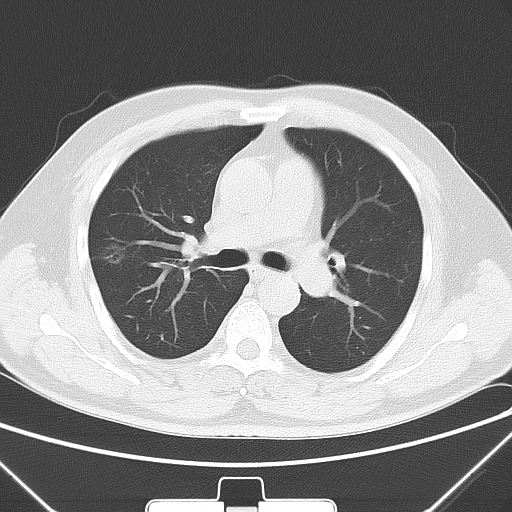
Chest CT, one axial slice; position 39 of 64 along the scan axis; lung window (W 1500 / L -600 HU); 5 mm slice thickness; 512 × 512 image matrix, field of view 350 × 350 mm. Patient: male, 58 years. Case-level facts recorded for this patient, not image findings: clinical TNM (as recorded): T1c N0 M0; histopathological grade: G2.
Structures marked on this image (rectangle marked by the reading radiologist):
- lung tumour (recorded histology: adenocarcinoma): box from (x=89, y=229) to (x=129, y=275) px